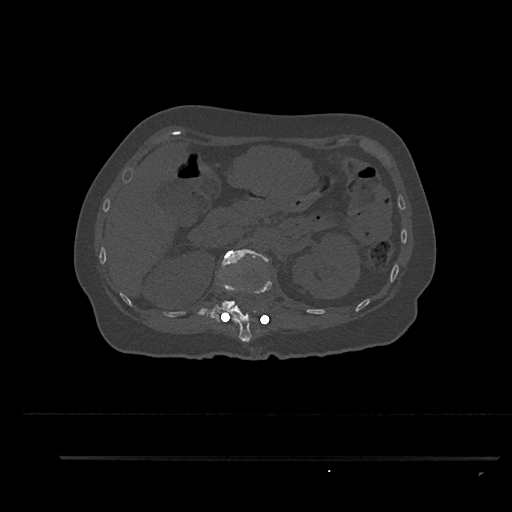
CT including the spine, one axial slice. Slice 237 of 797 in the series (ordered by position). Reconstruction kernel Br40s/3. 120 kVp. Bone window (W 1800 / L 400 HU). 512 × 512 image matrix, field of view 408 × 408 mm. Patient: female, 44 years. From the clinical record (not read from this slice): primary cancer: renal; vertebrae with lytic lesions (as recorded): L1.
Structures marked on this image (semi-automatic segmentation, software-assisted and operator-edited):
- L1 vertebra: bounding box [x1, y1, x2, y2] px = [209, 249, 269, 319]
- T12 vertebra: [213, 257, 272, 344]